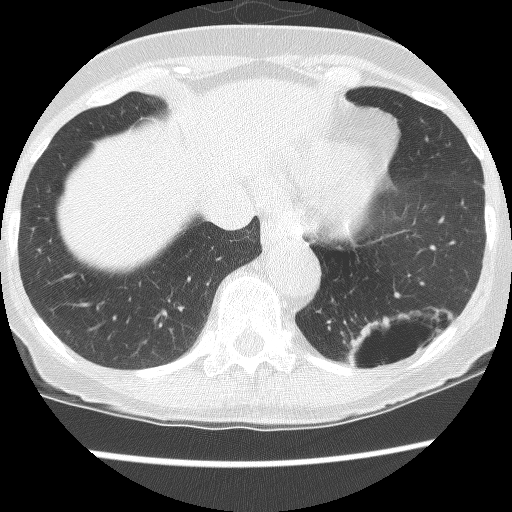
Low-dose screening chest CT, axial slice. Third annual screen. Lung window (W 1500 / L -600 HU). 2.5 mm slice thickness. 120 kVp. Slice 99 of 130 in the series. 512 × 512 image matrix, field of view 290 × 290 mm. Female, age 61 years at enrolment. Current smoker at enrolment.
- Expert reader's lesion annotation, bounding box <334,294,442,386> (left, top, right, bottom; pixels).
- The screening reader recorded 2 non-calcified nodules or masses ≥4 mm on this exam (left lower lobe, left lower lobe); which of them this box marks is not recorded.
- Official screen result: positive, no significant change: stable abnormalities potentially related to lung cancer, unchanged since the prior screening exam.
- Later outcome: lung cancer diagnosed 166 days after this screen — non-small cell carcinoma, left lower lobe, poorly differentiated (G3), stage IB (AJCC 6th edition), 100 mm at pathology.